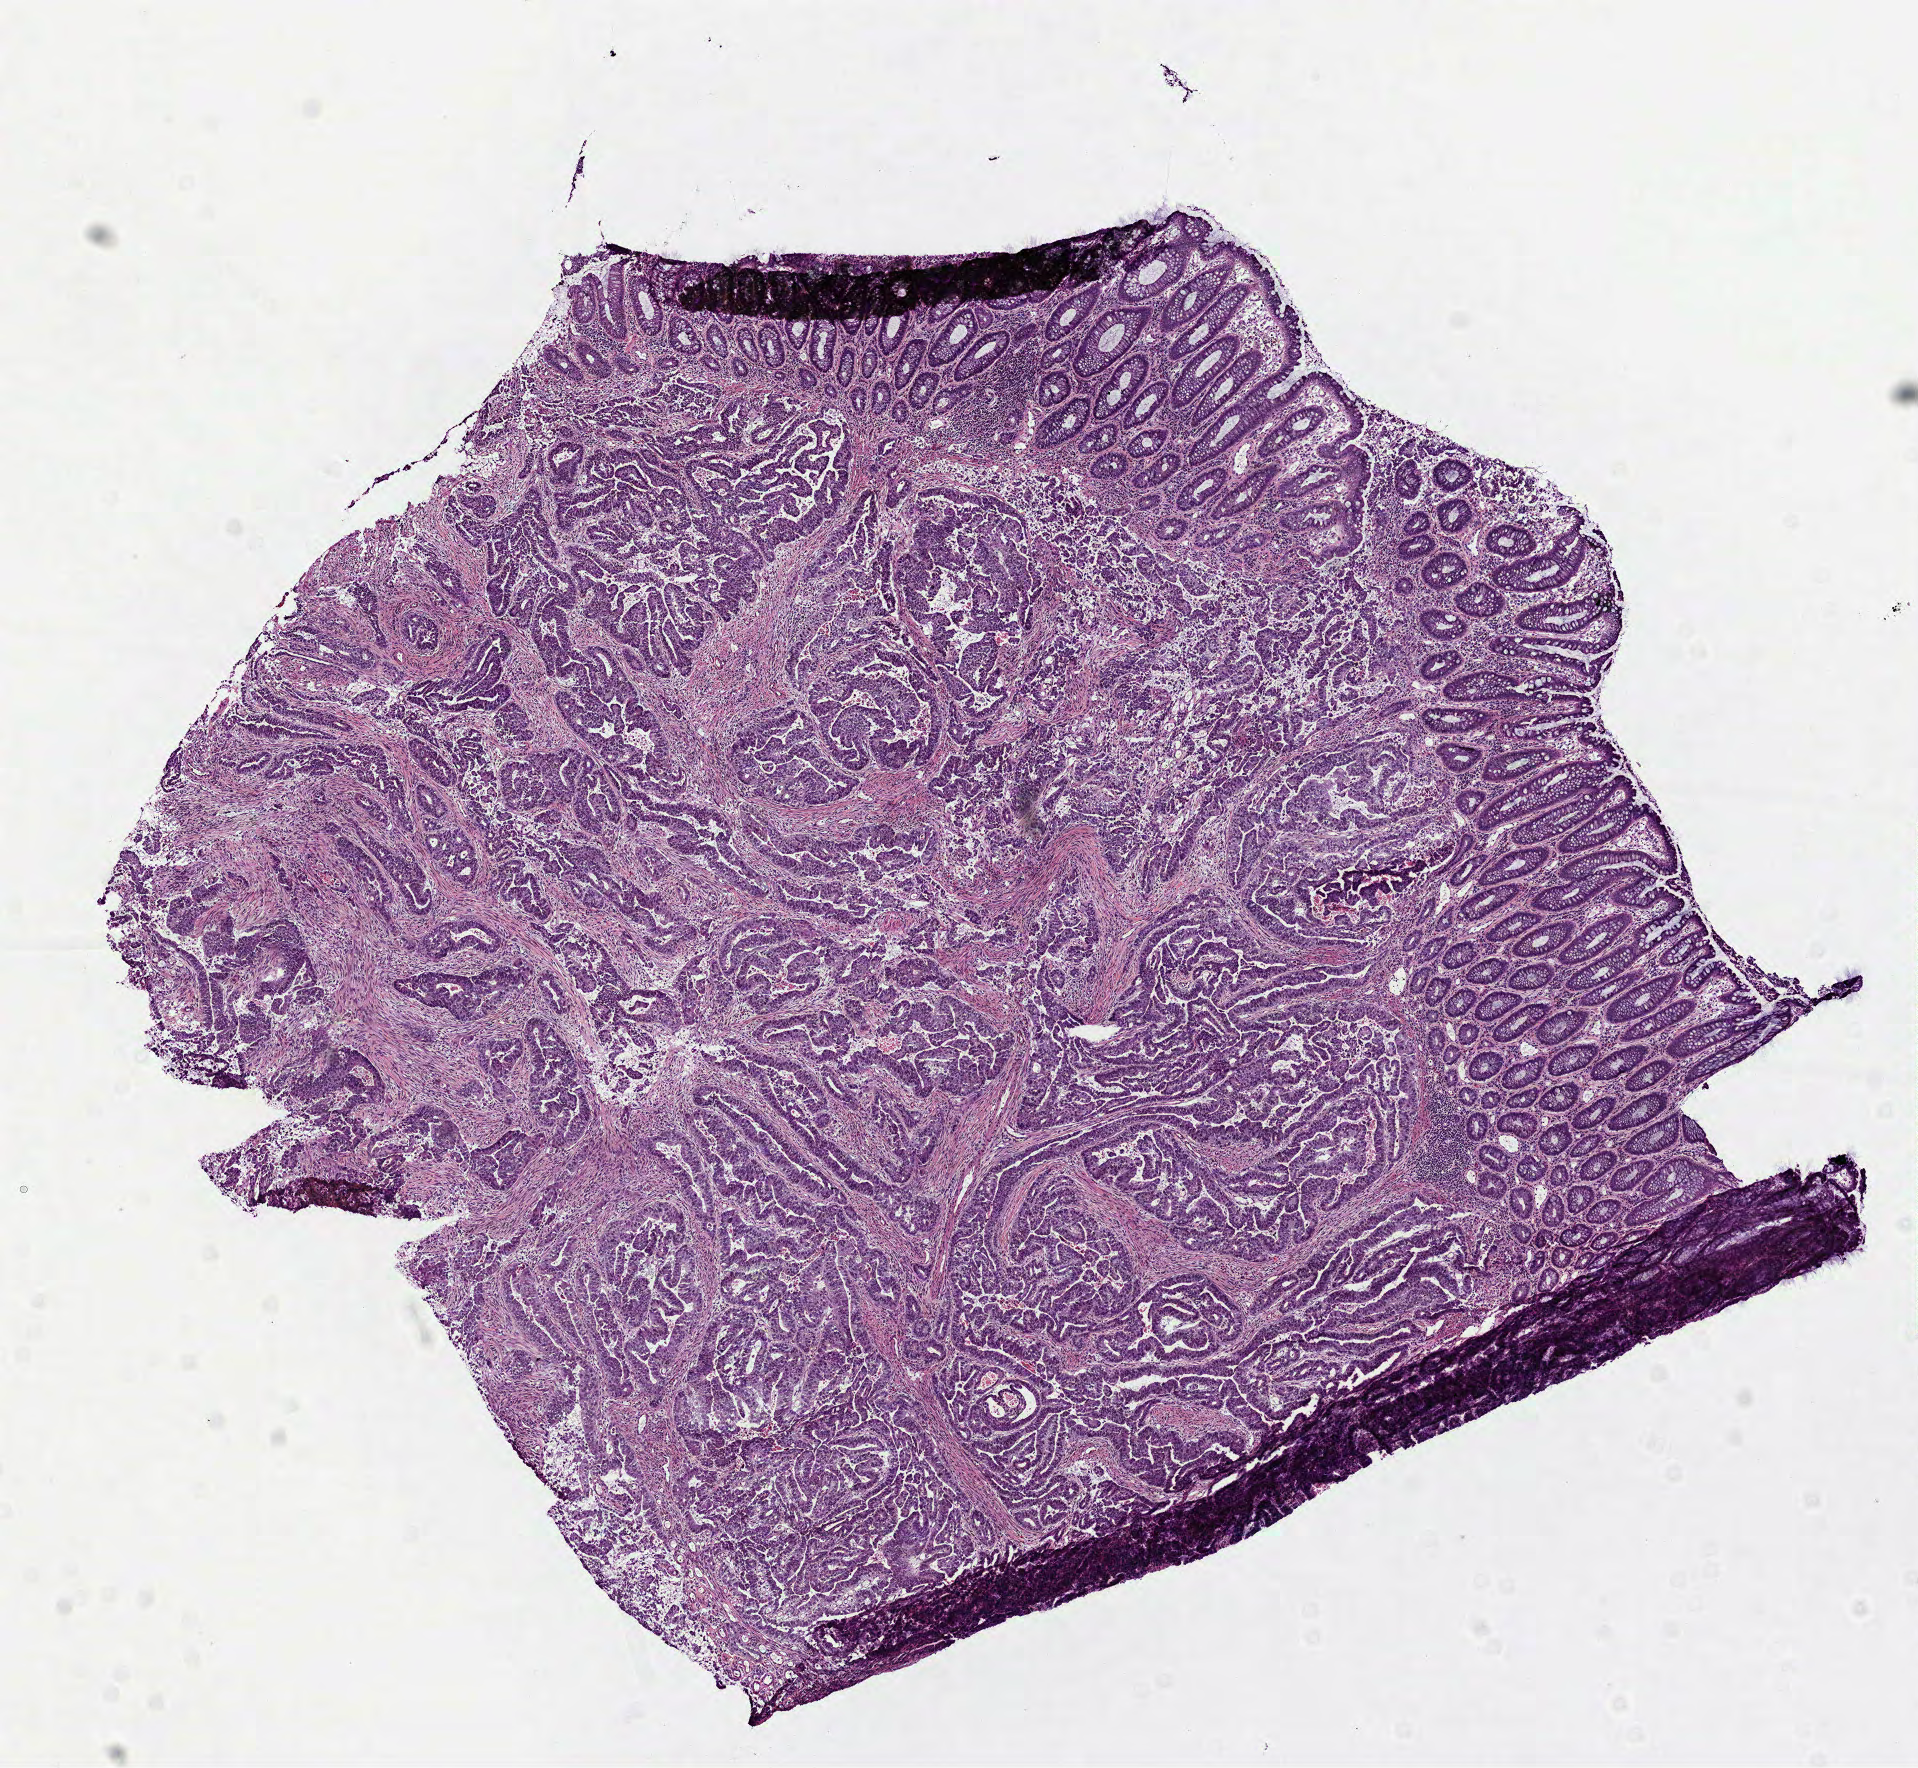
Whole-slide histology image, H&E-stained, whole scanned area (about 7.7 x 7.1 mm) shown as a low-resolution overview; frozen section from the top of the tissue portion; rectum, primary tumour sample. Male, age 72 years at initial diagnosis. Composition of this section per pathologist review: tumour cells 75%, tumour nuclei 80%, normal cells 24%, stromal cells 0%, necrosis 1%. Inflammatory infiltration, as recorded: lymphocyte infiltration 10%, monocyte infiltration 2%, neutrophil infiltration 5%.
• TNM: T3 N1 MX
• histologic diagnosis: Adenocarcinoma, NOS (rectosigmoid junction)
• AJCC pathologic stage: IIIB (6th edition)
• lymph nodes positive (case pathology): 1 of 13 examined